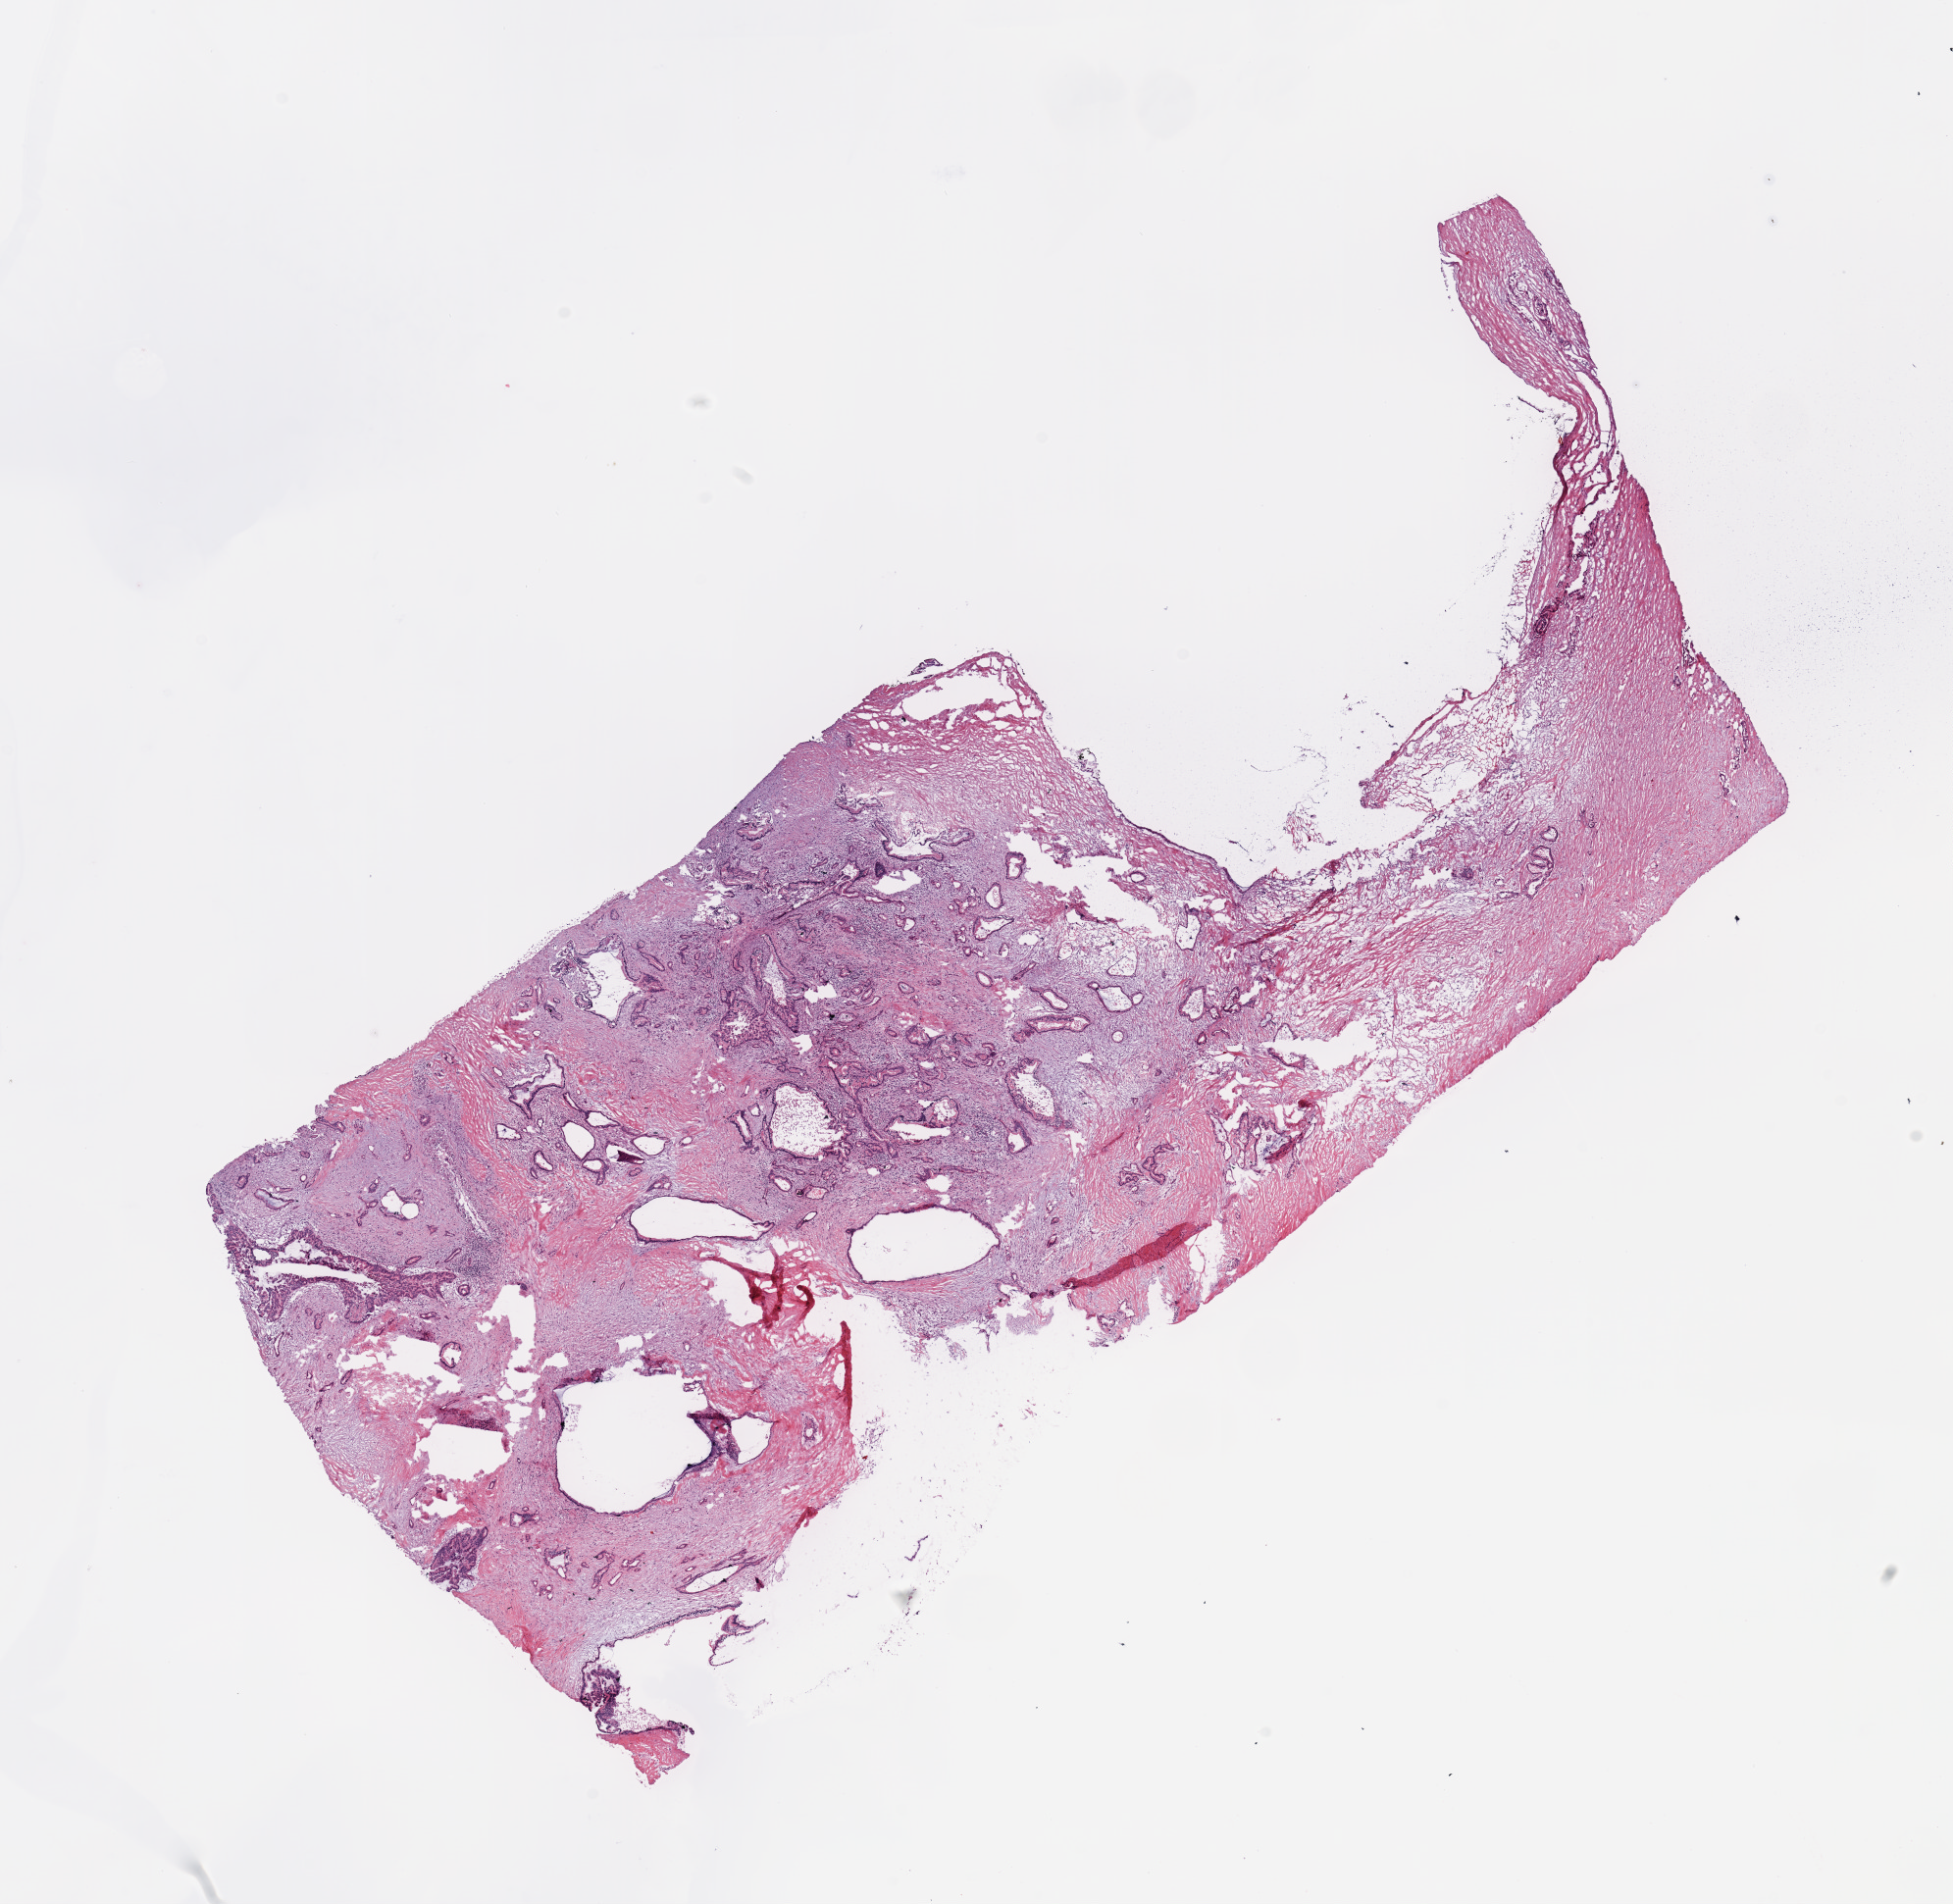
Digitized H&E-stained tissue section (whole slide), low-resolution overview of the scanned area, about 15.8 x 15.4 mm (acquisition: 20x scan); tumour tissue sample, pancreas. Male, 69 y/o.
Histologic diagnosis: Infiltrating duct carcinoma, NOS.